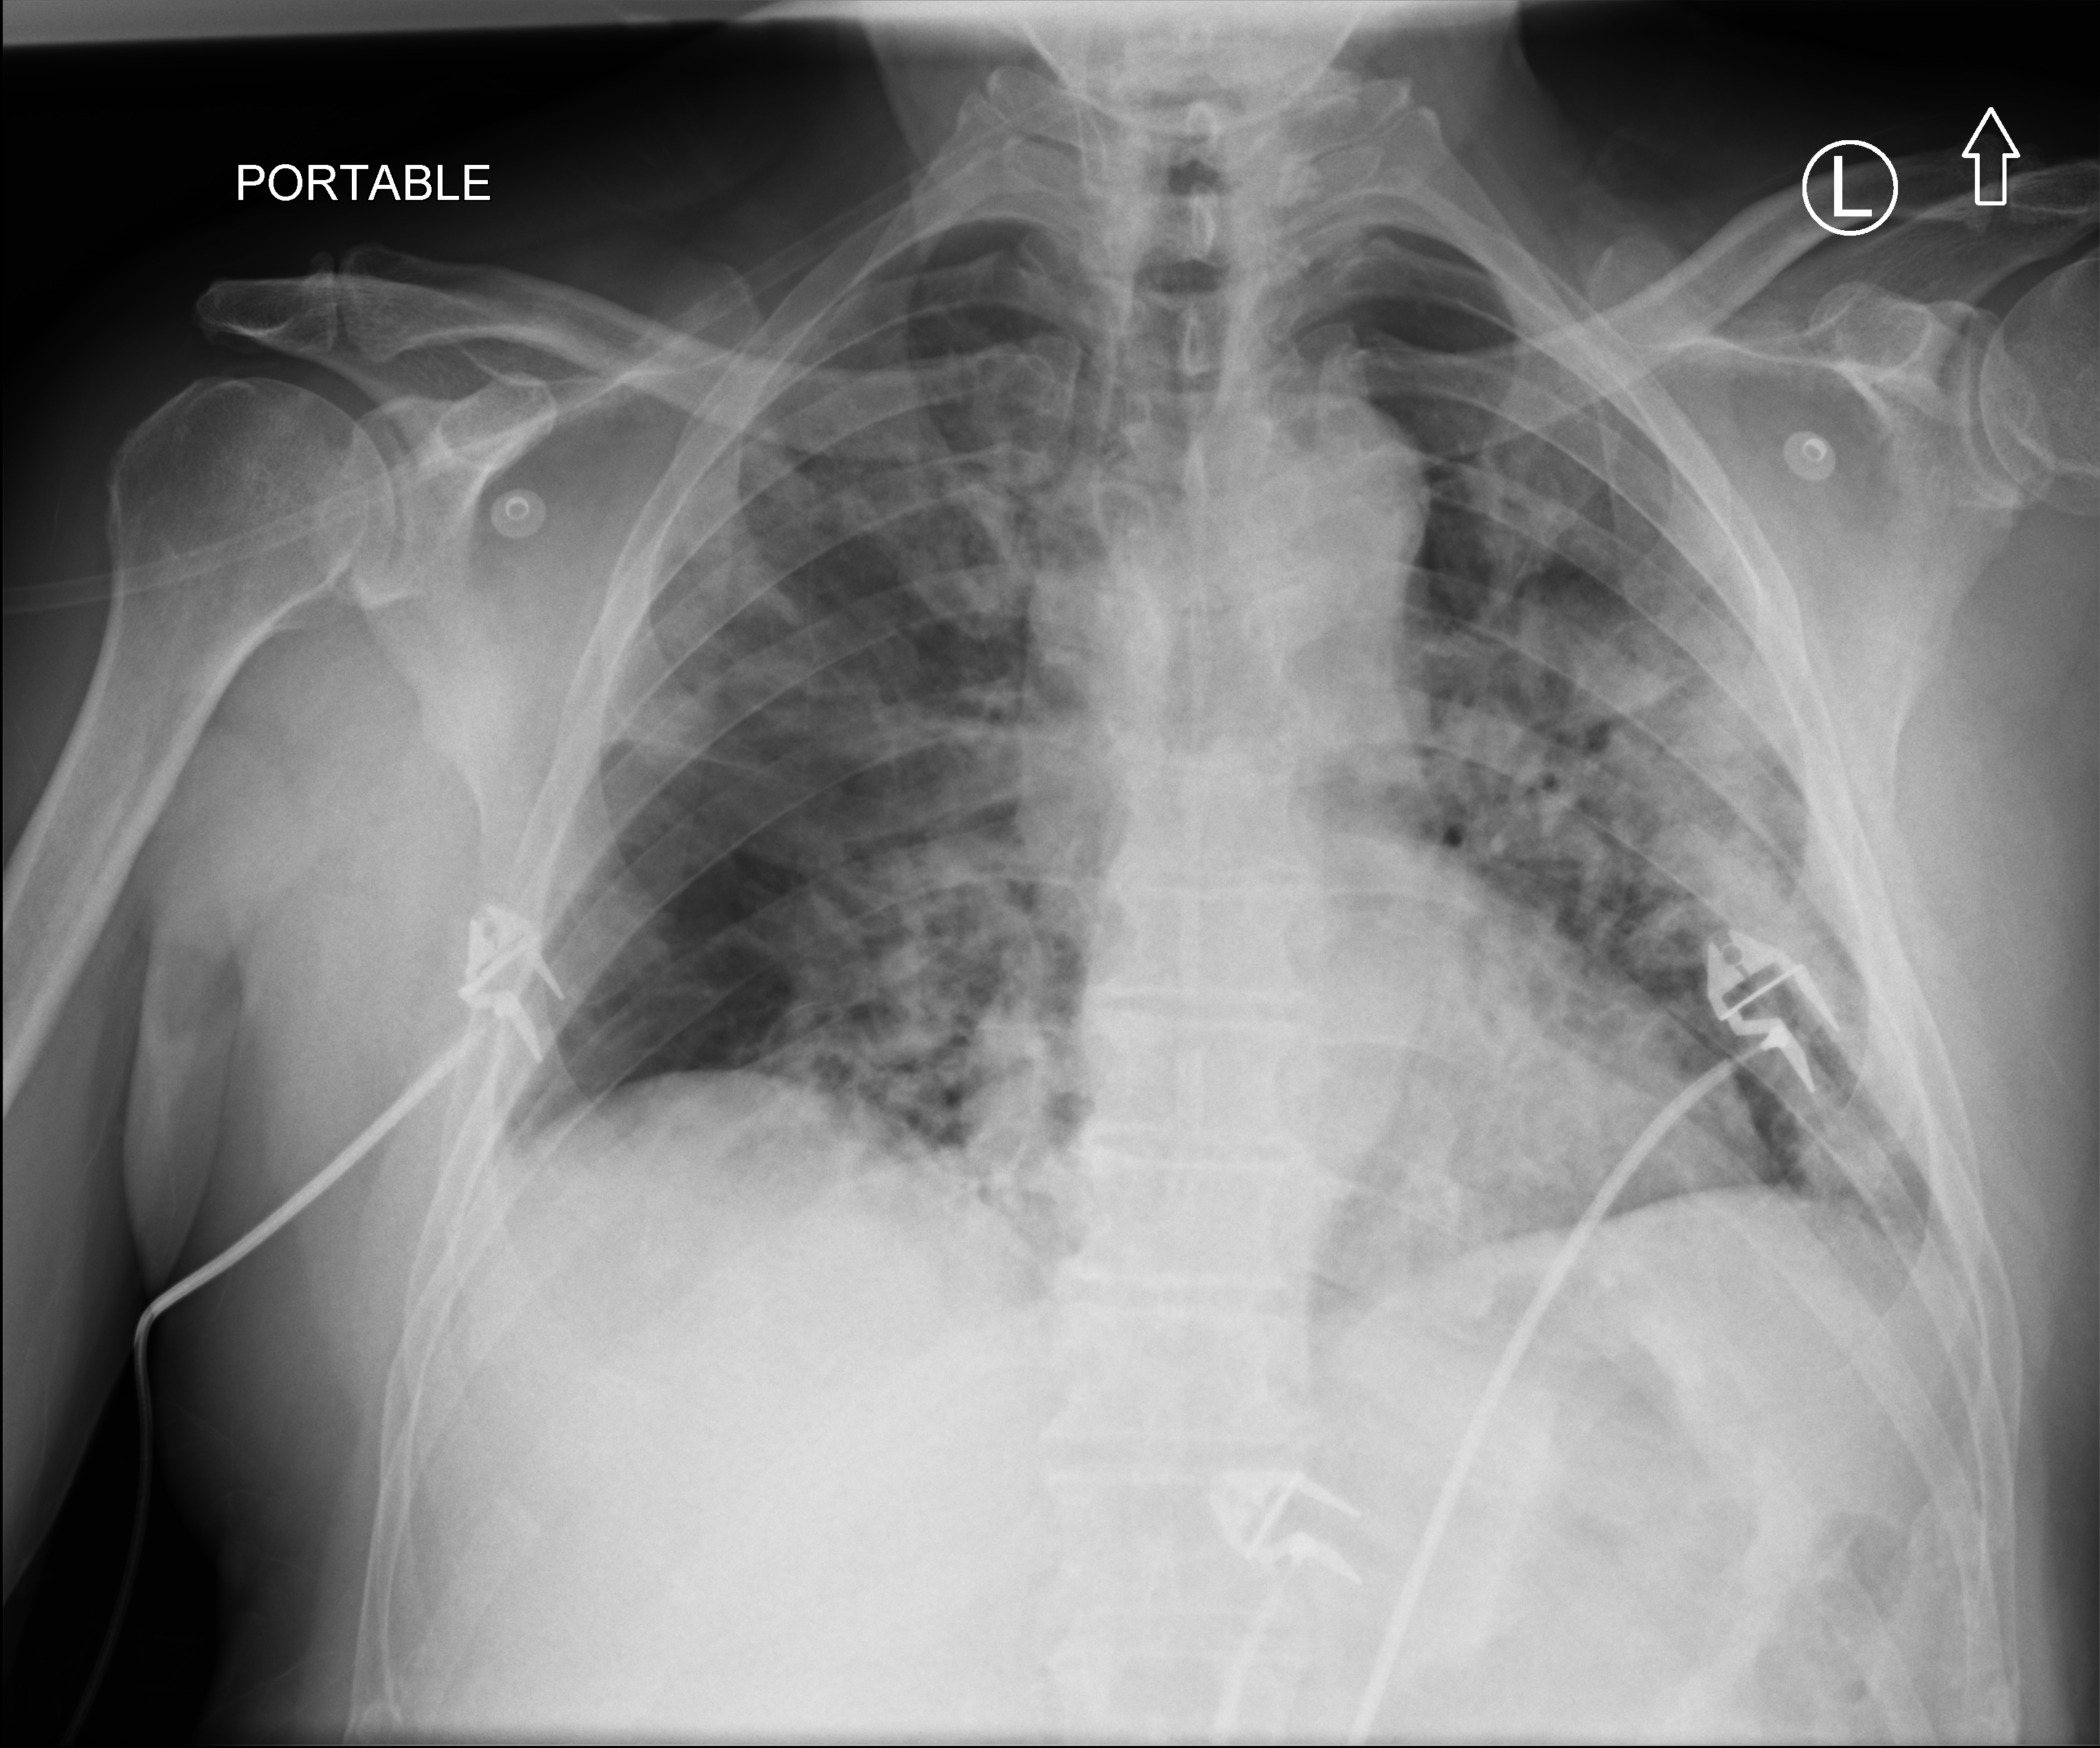
Chest X-ray (portable), anteroposterior (AP) projection. Patient hospitalised with COVID-19; male, aged 60–74 years.
From the hospital-stay record, not from the radiograph (when in the stay this image was taken is not recorded):
- mechanically ventilated during this hospital stay: yes
- admitted to intensive care during this hospital stay: yes
- hypertension (admission record): yes